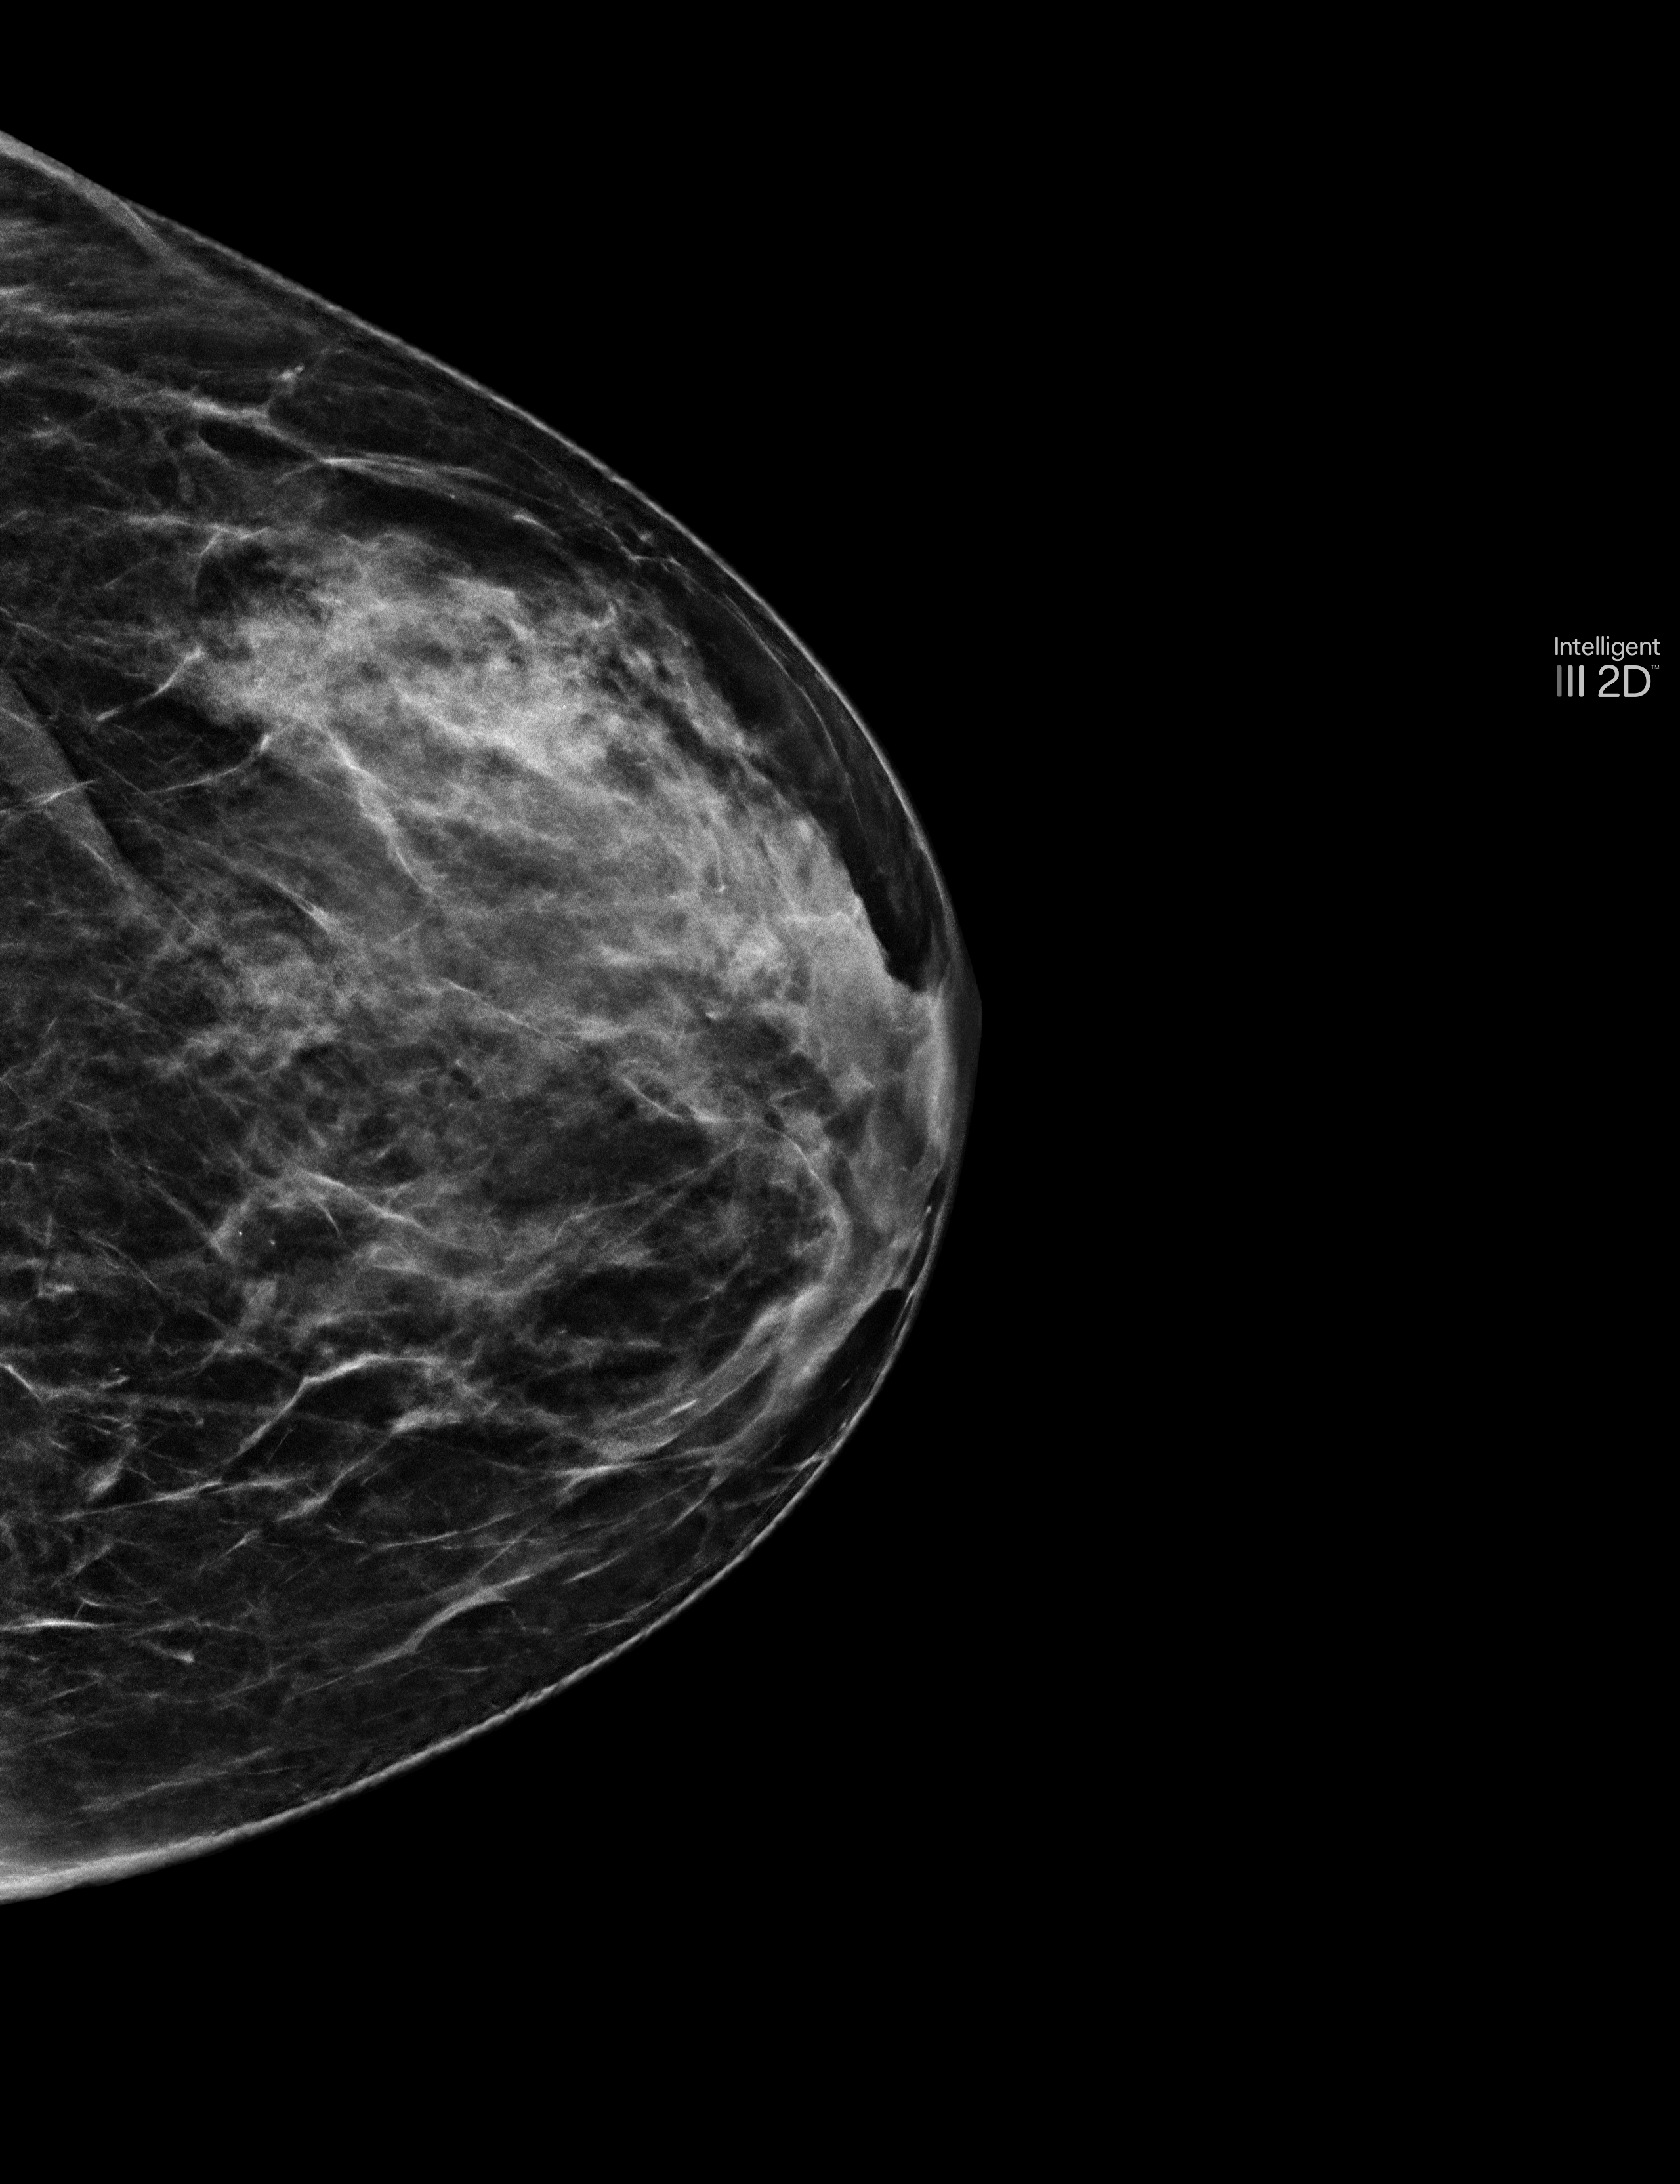
Screening examination, system: Selenia Dimensions. Patient: female, 51 years.
Image type: synthesized 2-D view from tomosynthesis. Breast: left. Projection: craniocaudal (CC) view.